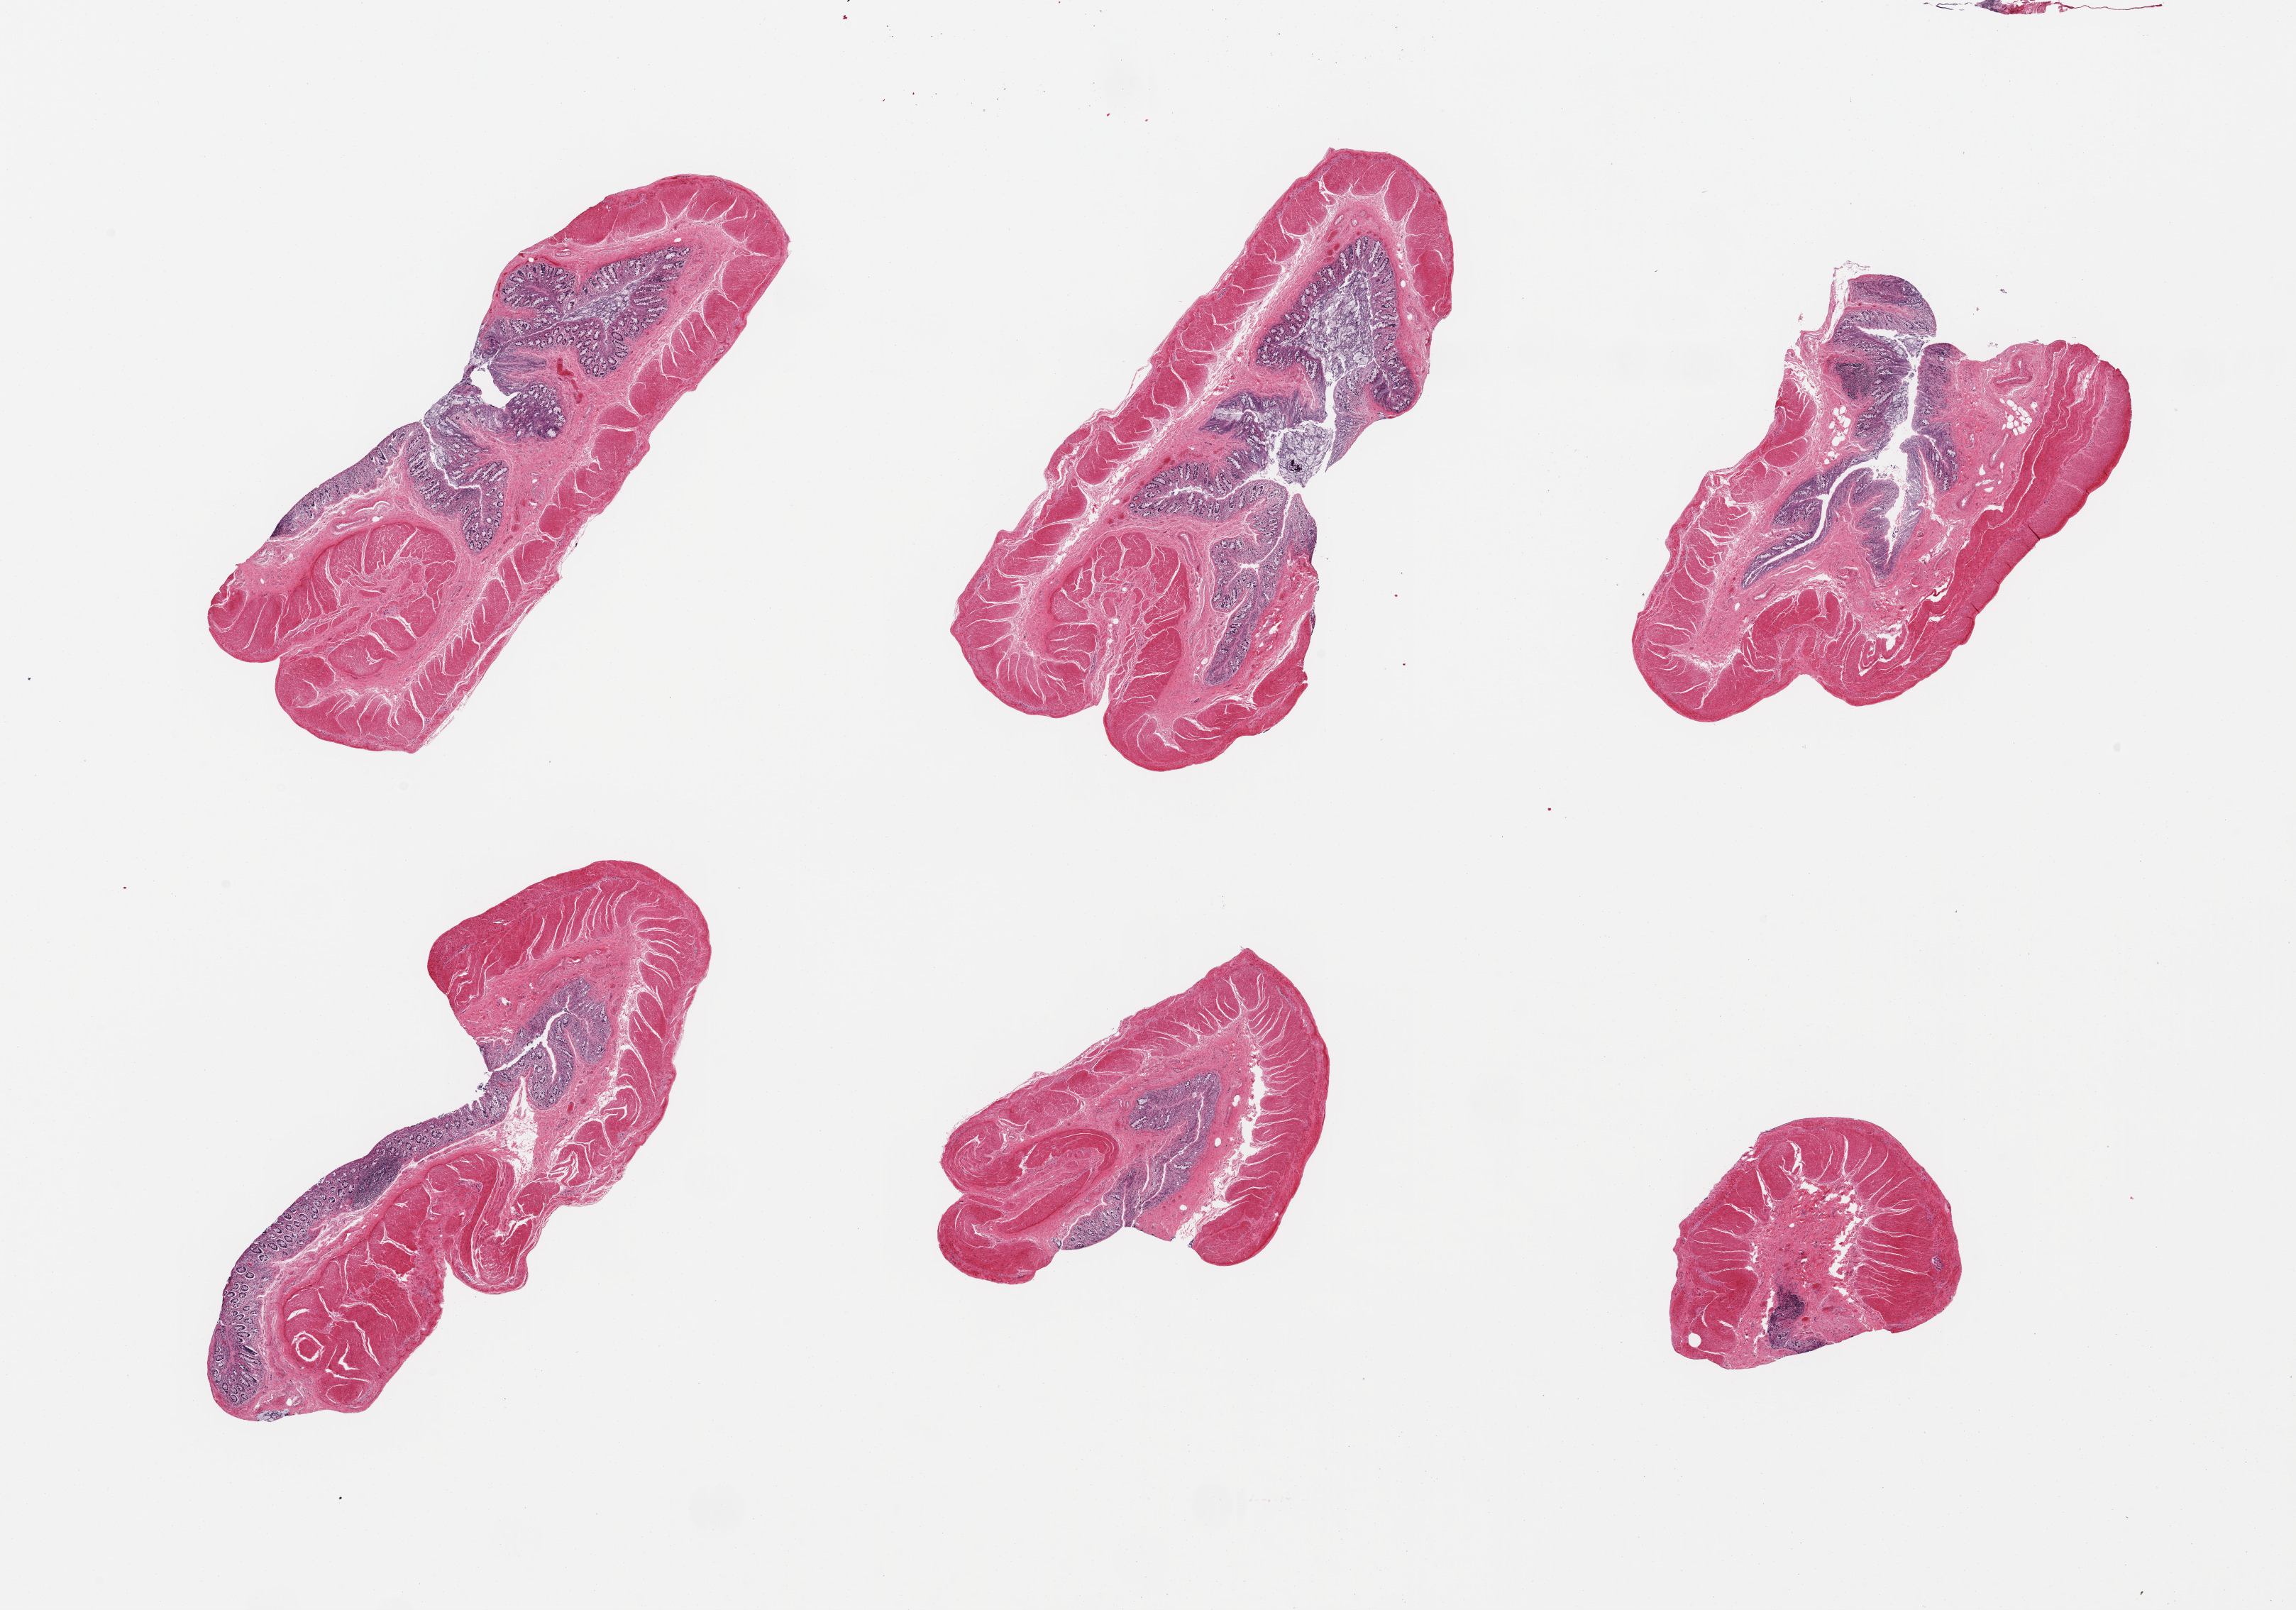
Digitized hematoxylin and eosin (H&E)-stained section, shown as a low-resolution overview of the whole scanned area (about 25.6 x 17.9 mm, slide scanned at 20x). PAXgene-fixed paraffin-embedded (PFPE) section. Section of transverse colon (target tissue). Tissue donor sample. Donor: male.
Reviewer comment on this tissue sample: 6 pieces, mucosa up to ~0.25mm, glandular elements sloughing.